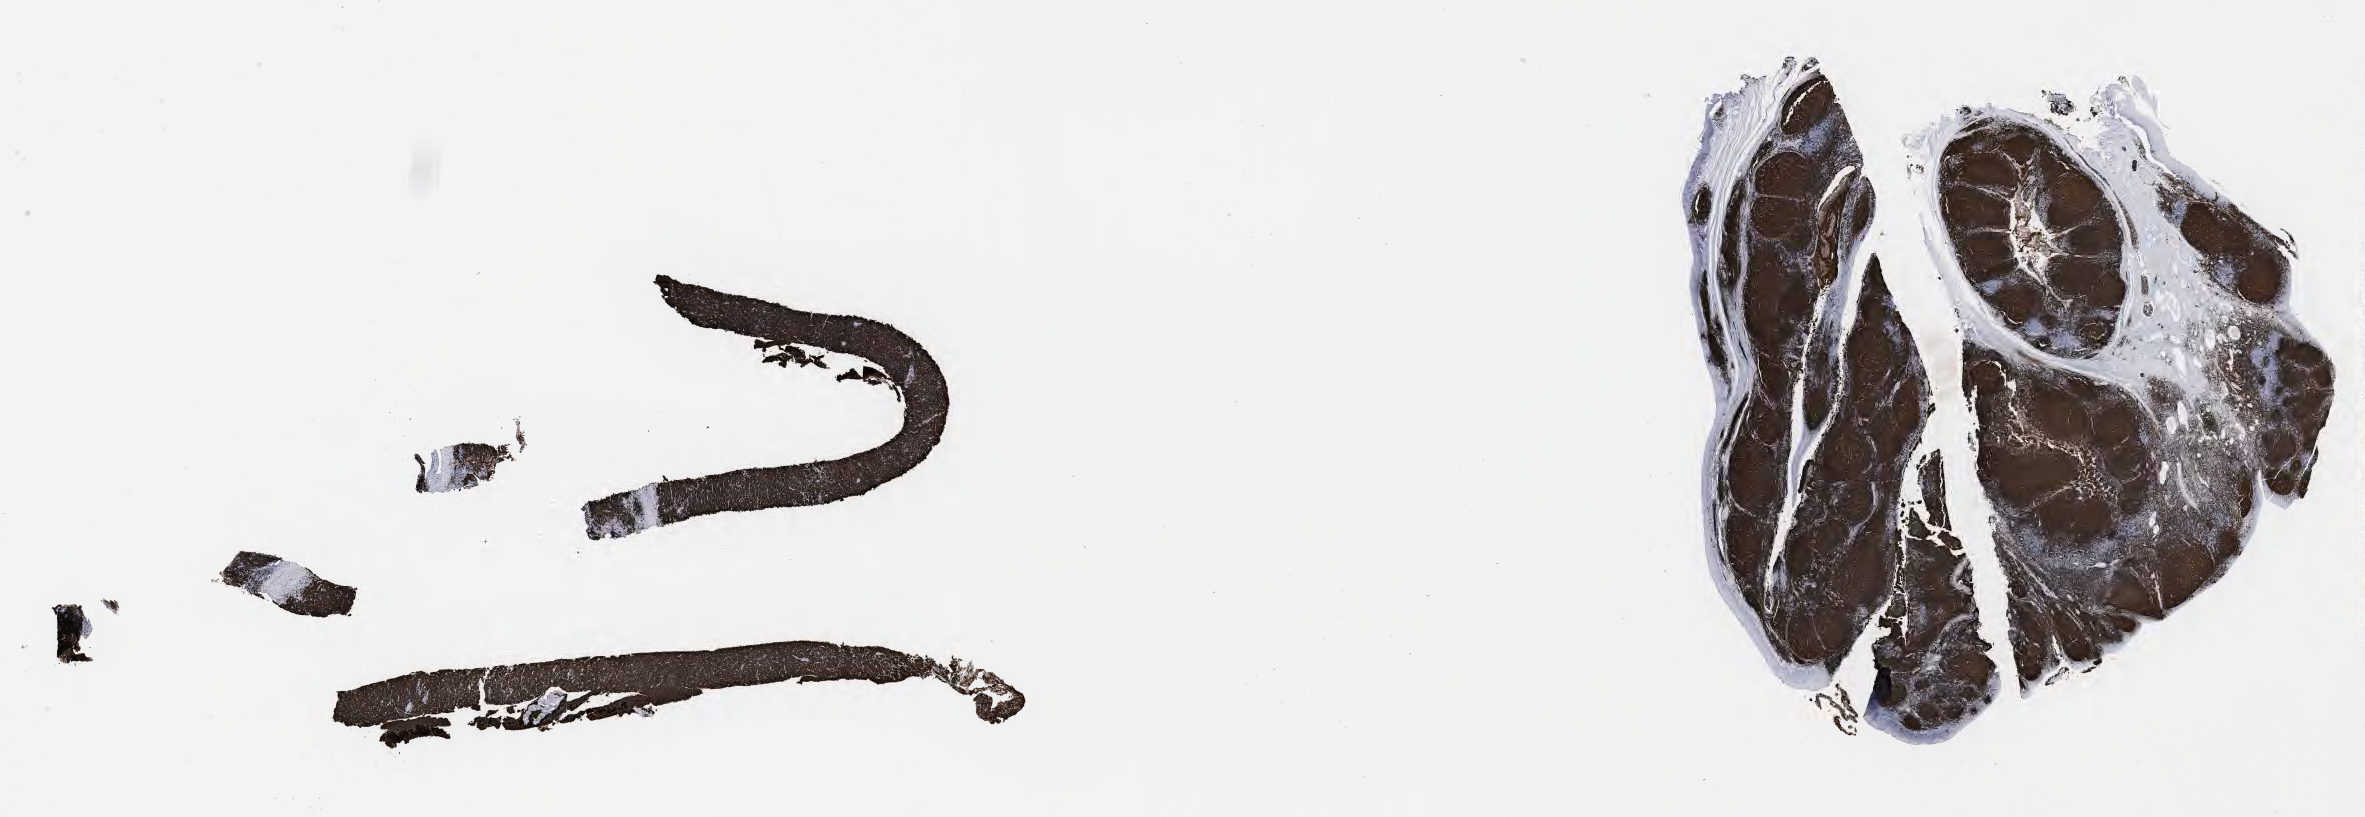
Whole-slide image, immunohistochemical stain for CD20 — a low-resolution overview of the entire scanned area, about 38.2 x 13.2 mm, tumor tissue. Patient: male, aged 55.
Diagnosis: Burkitt lymphoma, NOS.